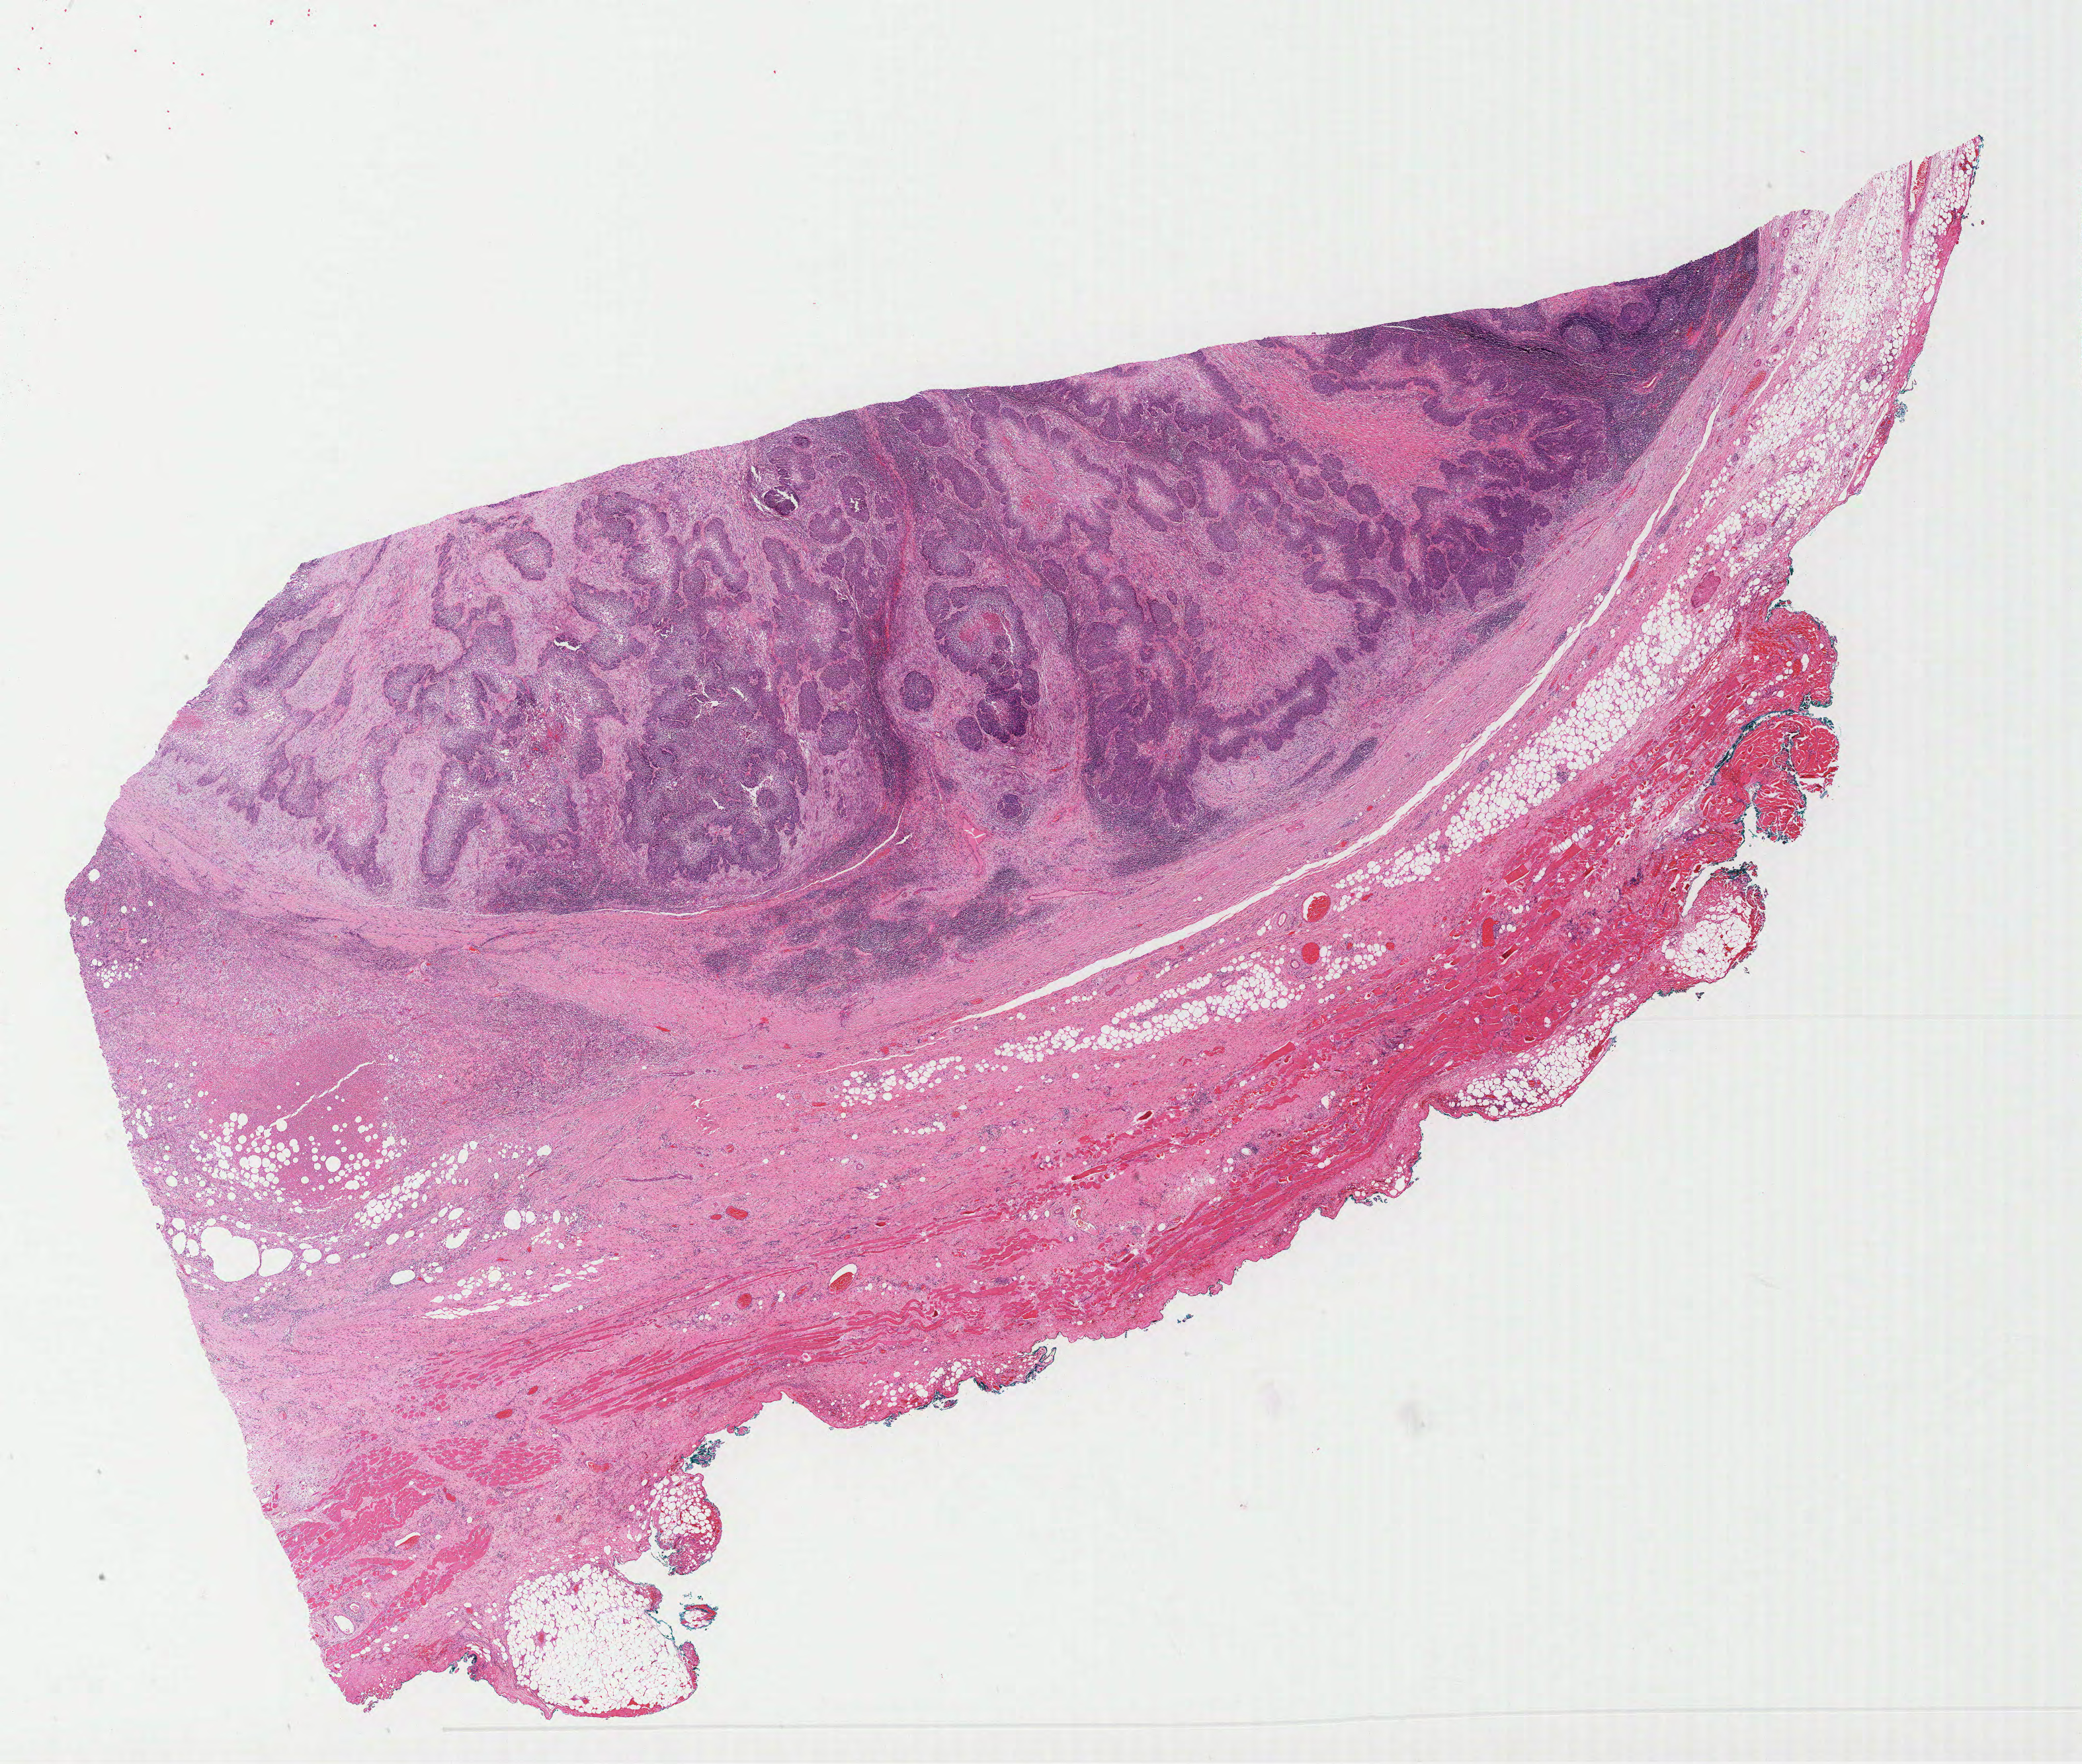
Whole-slide histology image, H&E, shown as a low-resolution overview of the whole scanned area (about 25.5 x 21.6 mm, acquisition: 40x scan); formalin-fixed paraffin-embedded (FFPE) diagnostic section; primary tumour sample from the head and neck. Male patient; age at initial diagnosis 56 years. Histologic grade: G3 (poorly differentiated).
TNM: T2 N2b M0. Pathologic diagnosis: Squamous cell carcinoma, NOS (floor of mouth, NOS). Laterality: right. AJCC pathologic stage: IVA (6th edition).